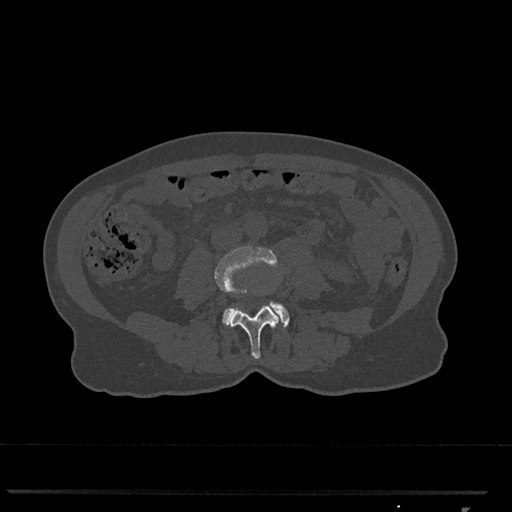
CT including the spine, one axial slice. Position 249 of 793 along the scan axis. 120 kVp. Bone window (W 1800 / L 400 HU). 0.5 mm slice thickness. 512 × 512 image matrix, field of view 380 × 380 mm. Patient: female, 62 years. Case-level facts recorded for this patient, not image findings: primary cancer: renal.
Annotated regions visible in this slice (semi-automatic segmentation, software-assisted and operator-edited):
- L3 vertebra: box from (x=214, y=246) to (x=282, y=359) px
- L4 vertebra: (x=223, y=301)–(x=290, y=327)